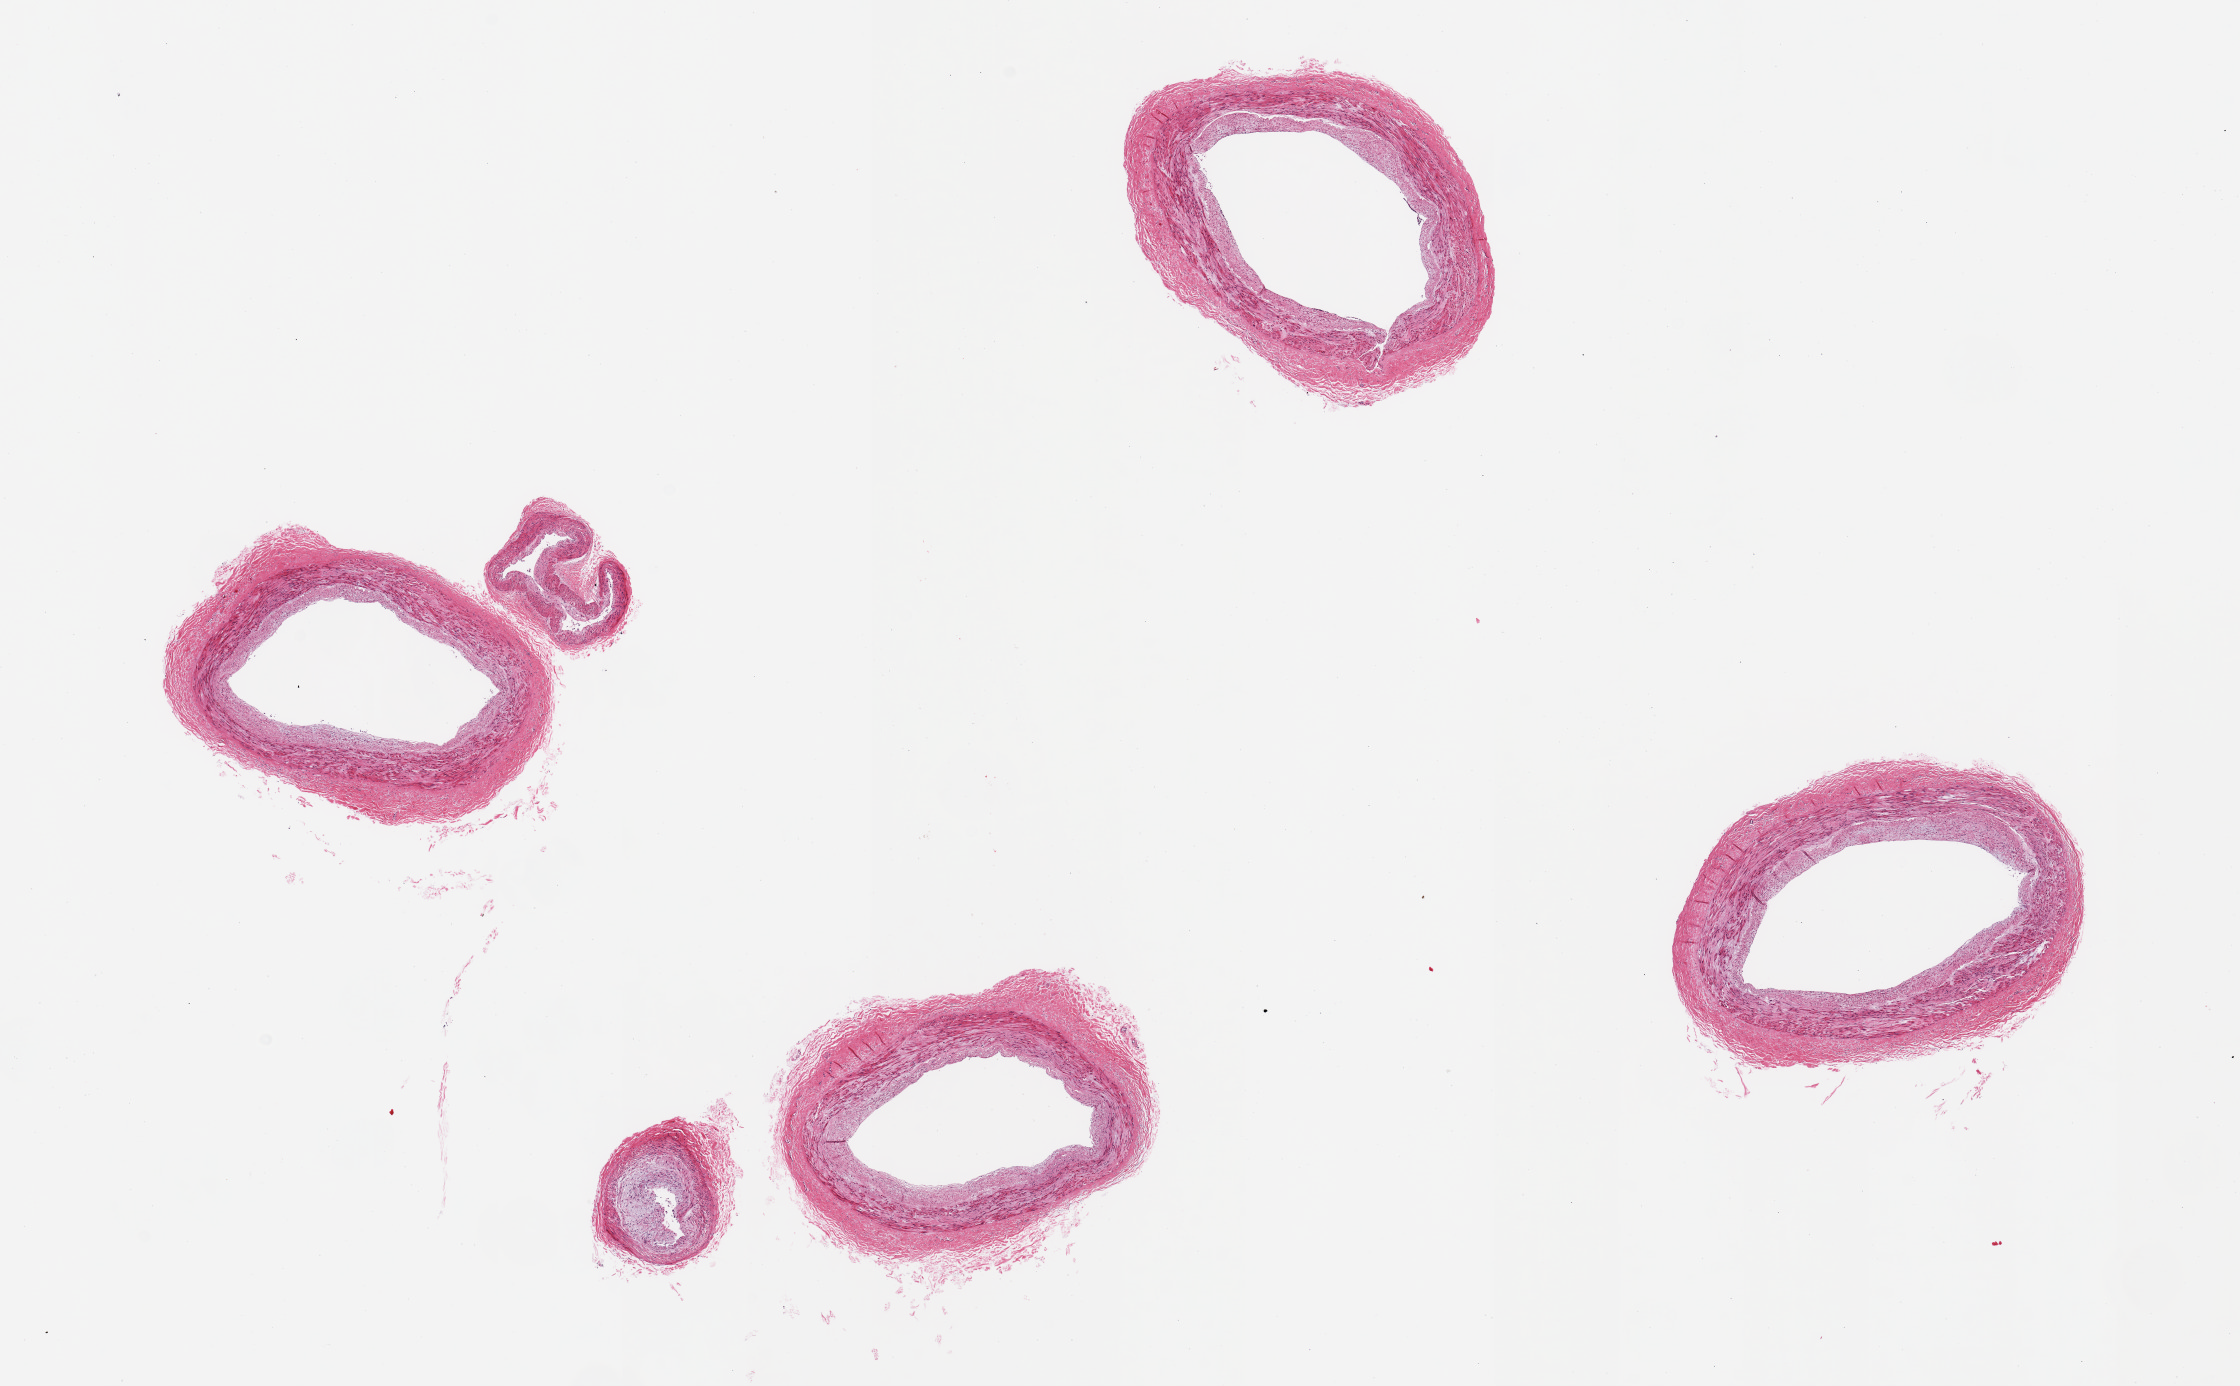
Hematoxylin and eosin (H&E) whole-slide image, brightfield — whole scanned area (about 17.7 x 11.0 mm, acquisition: 20x scan) shown as a low-resolution overview, PAXgene-fixed, paraffin-embedded tissue, sampled site (target tissue): tibial artery, tissue donor sample. Donor: female.
• pathologist's review note for this sample: 4 pieces; mild intimal fibrosis; 2 small branches also present